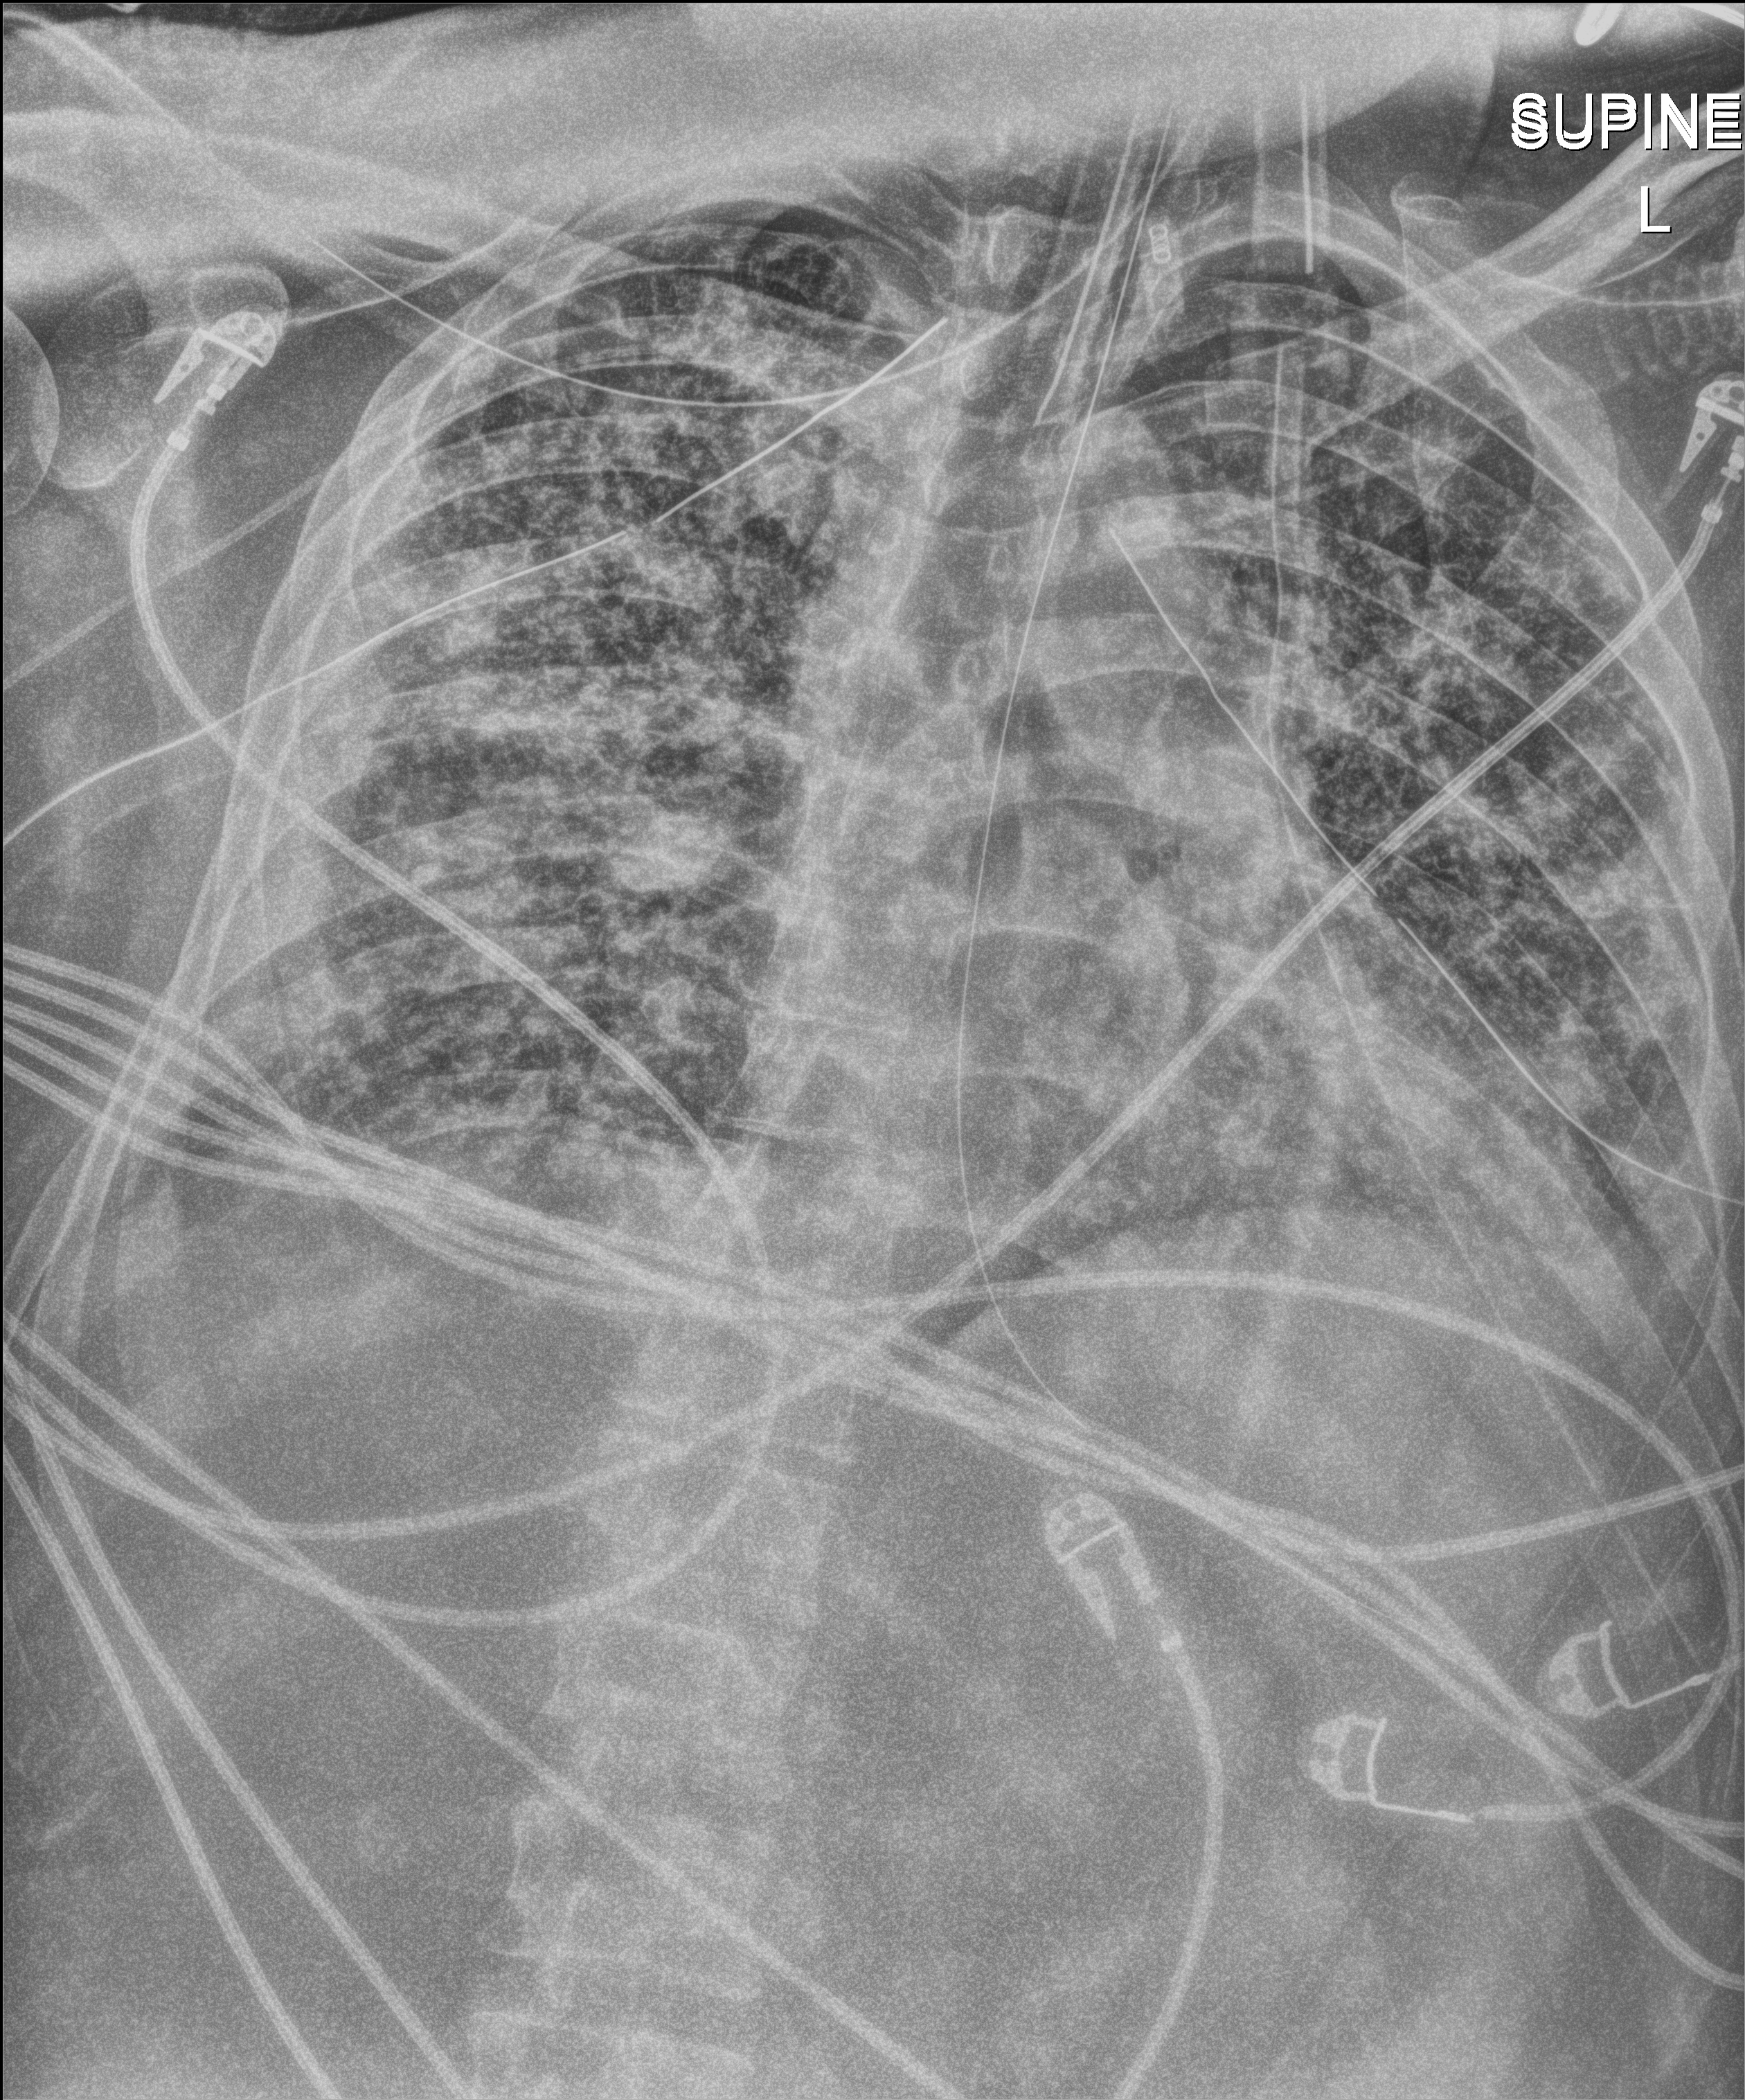
Chest X-ray (portable), anteroposterior (AP) projection. Patient hospitalised with COVID-19; male, aged 18–59 years.
Admission-level facts for this patient (not findings on this image; timing relative to this image not recorded): length of hospital stay: 63 days; mechanically ventilated during this hospital stay: yes; admitted to intensive care during this hospital stay: yes.